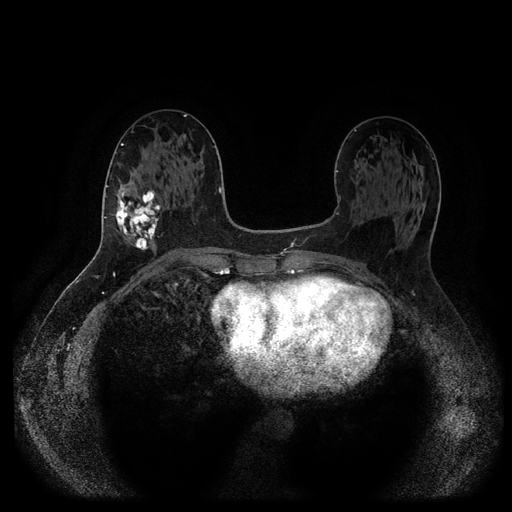
Breast MRI (dynamic contrast-enhanced, multi-phase), one axial slice. Slice 47 of 116 in the series (ordered by position). Dynamic contrast-enhanced series, time point 2 of 5 at this slice position (early post-contrast). 1.5 T. TE 2.6 ms, TR 5.3 ms. 2 mm slice thickness. 512 × 512 image matrix, field of view 360 × 360 mm. Female patient, age 58 years.
Annotated regions visible in this slice (semi-automatically segmented with operator editing):
- breast lesion (labelled 'tumour' in the annotation; benign lesions carry a separate 'benign' label): bounding box [x1, y1, x2, y2] px = [113, 185, 162, 252]